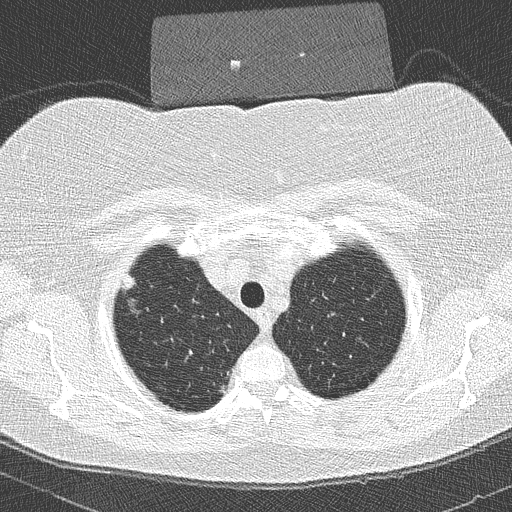
Chest CT (low-dose screening protocol), one axial image; second annual screen; lung window (W 1500 / L -600 HU); 2 mm slice thickness; lung (sharp) reconstruction kernel (B50f); slice 33 of 293 in the series; 512 × 512 image matrix, field of view 320 × 320 mm. Female, age 58 years at enrolment.
Lesion marked by an expert reader, bounding box [x1, y1, x2, y2] px = [111, 269, 148, 311]. The screening reader recorded 2 non-calcified nodules or masses ≥4 mm on this exam; which of them this box marks is not recorded. Official screen result: positive, other.